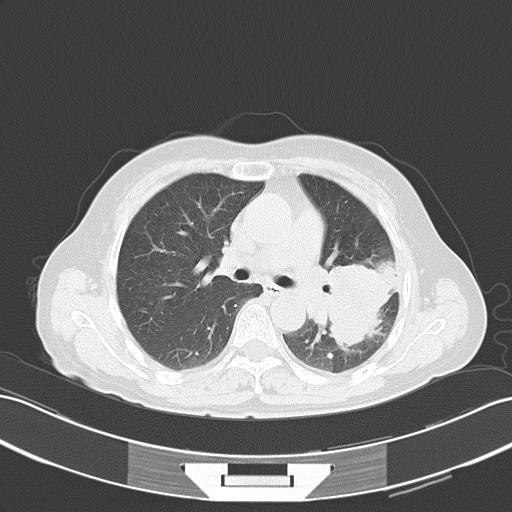
Chest CT, one axial slice. Position 31 of 51 along the scan axis. 120 kVp. Lung window (W 1500 / L -600 HU). 512 × 512 image matrix, field of view 353 × 353 mm. Female patient, age 54 years. From the clinical record (not read from this slice): clinical TNM (as recorded): T3 N1 M0.
Annotated regions visible in this slice (rectangle marked by the reading radiologist):
- lung tumour (recorded histology: adenocarcinoma): bounding box [x1, y1, x2, y2] px = [319, 250, 395, 355]